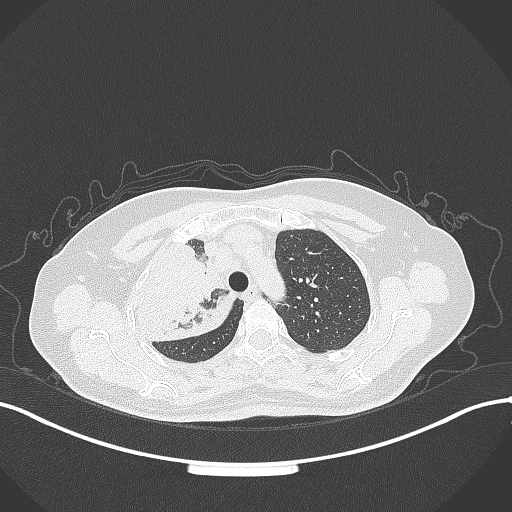
Chest CT, one axial slice. Position 246 of 309 along the scan axis. Reconstruction kernel B70f. 120 kVp. Lung window (W 1500 / L -600 HU). 1 mm slice thickness. 512 × 512 image matrix, field of view 400 × 400 mm. Female patient, age 60 years. From the clinical record (not read from this slice): clinical TNM (as recorded): T3 N1 M1.
Structures marked on this image (rectangle marked by the reading radiologist):
- lung tumour (recorded histology: adenocarcinoma): bounding box <123,236,238,345> (left, top, right, bottom; pixels)